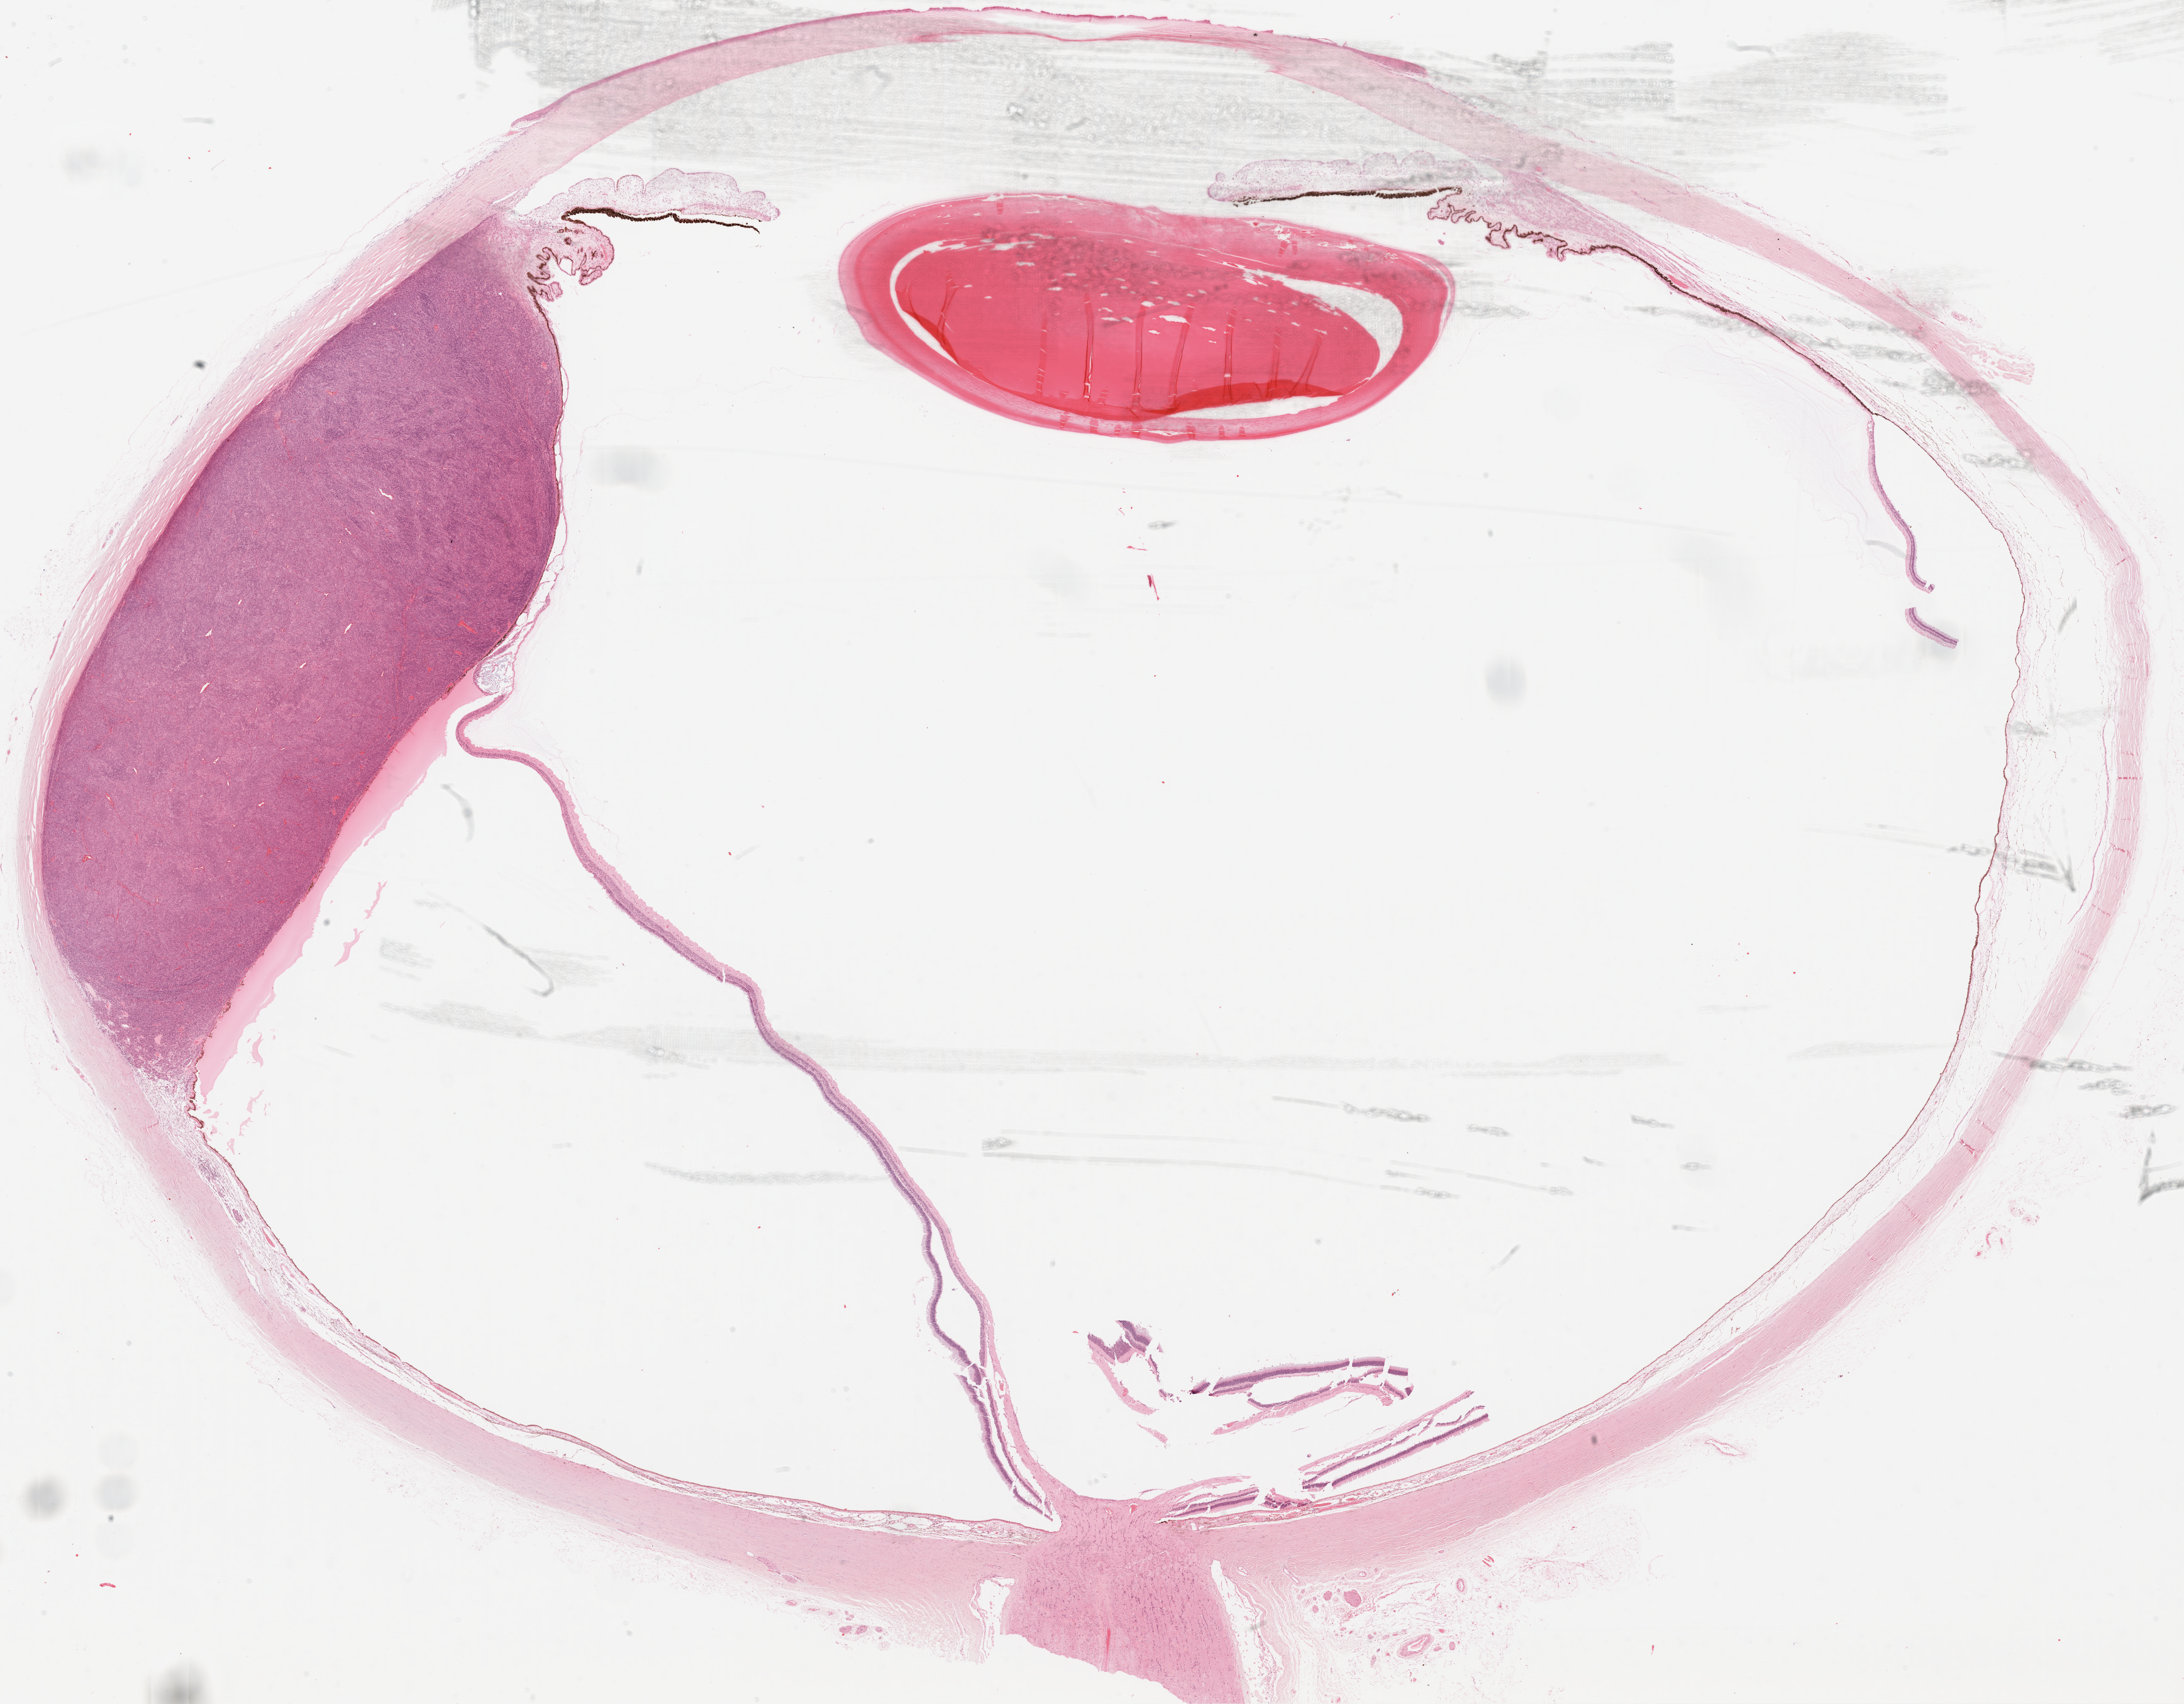
Digitized H&E tissue section (whole slide) — whole scanned area (about 28.0 x 21.9 mm, slide scanned at 20x) shown as a low-resolution overview; formalin-fixed paraffin-embedded (FFPE) diagnostic section; primary tumour sample from the uvea. Male, age 68 years at initial diagnosis.
Pathologic diagnosis: Mixed epithelioid and spindle cell melanoma (overlapping lesion of eye and adnexa).